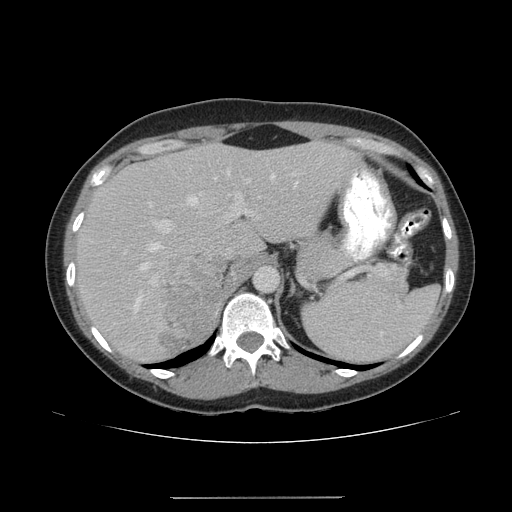
Contrast-enhanced abdominal CT, one axial slice; position 121 of 161 along the scan axis; intravenous contrast given; soft-tissue window (W 400 / L 40 HU); 3.75 mm slice thickness; 512 × 512 image matrix, field of view 380 × 380 mm. Female patient. From the clinical record (not read from this slice): diagnosis: adrenocortical carcinoma; tumour side: right adrenal; tumour size at pathology: 9 cm; Ki-67 index: 14 %; stage (as recorded): 3.
Annotated regions visible in this slice (semi-automatic segmentation, software-assisted and operator-edited):
- mass: bounding box <160,255,265,354> (left, top, right, bottom; pixels)